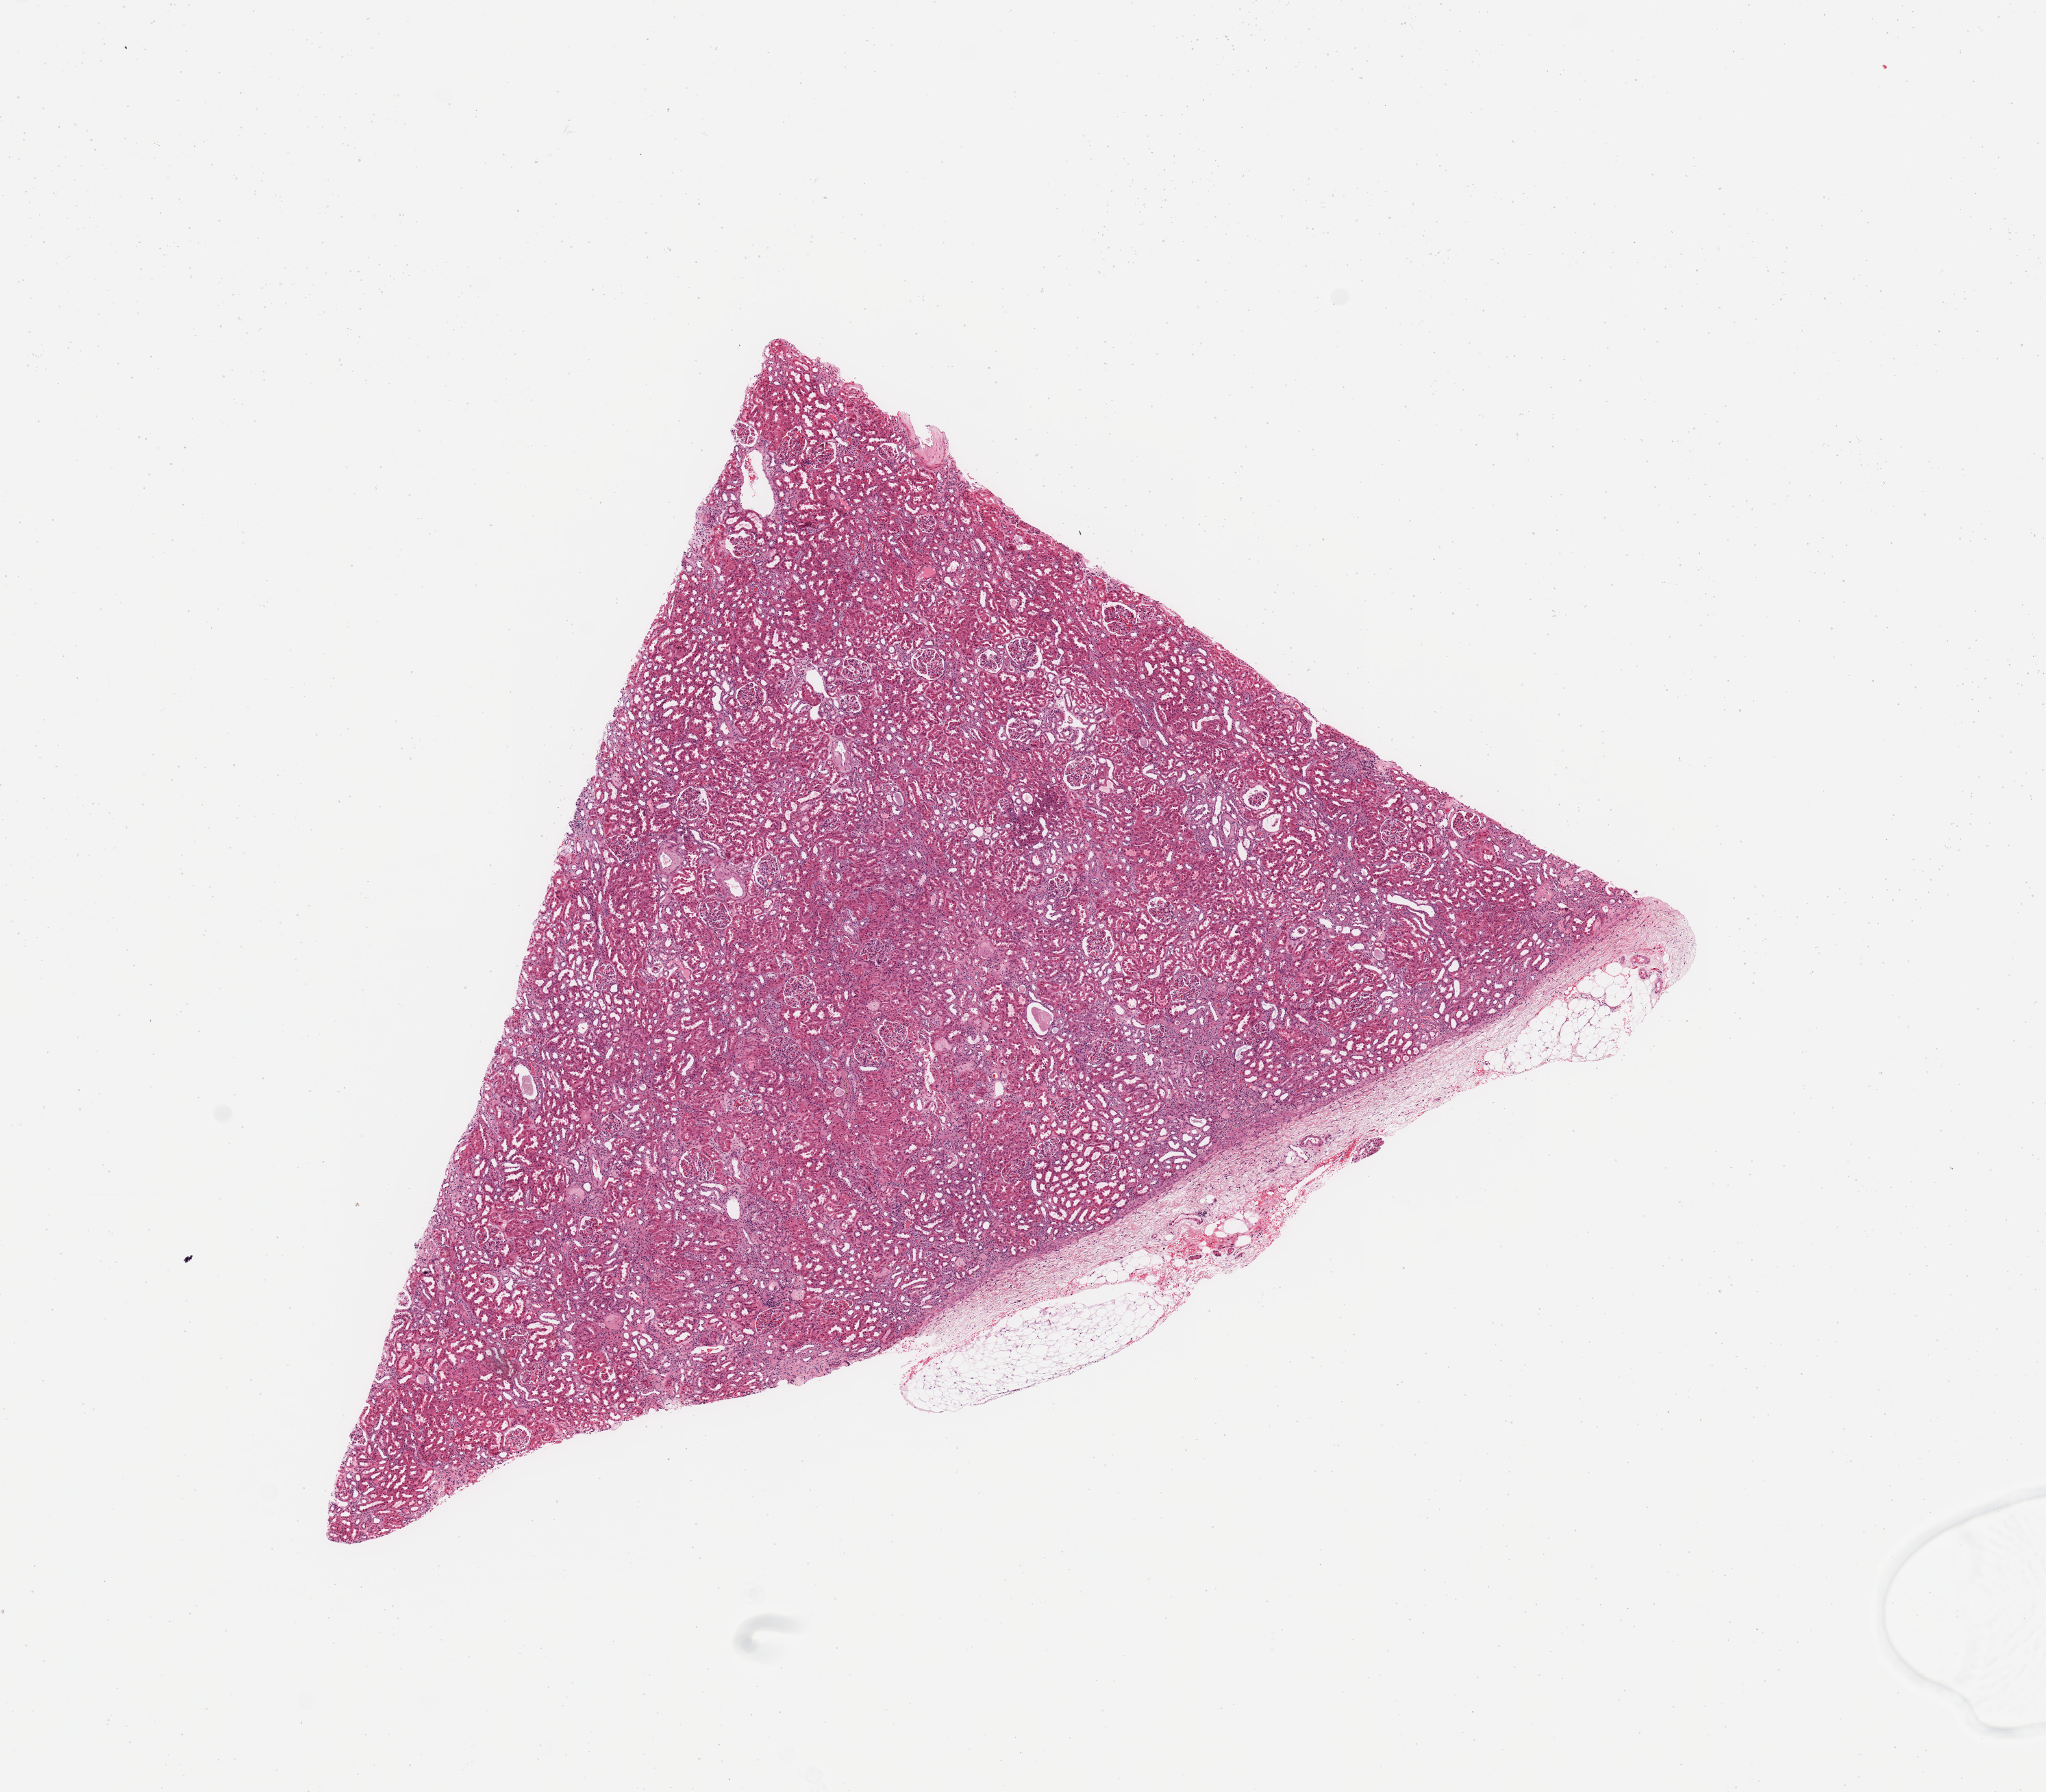
Whole-slide histology image, H&E-stained — shown as a low-resolution overview of the whole scanned area (about 11.8 x 10.3 mm), normal (non-tumour) tissue sample, sampled site: kidney. Patient: female, age 71 years.
This section: normal (non-tumour) tissue from the same patient. Patient diagnosis: Renal cell carcinoma, NOS.